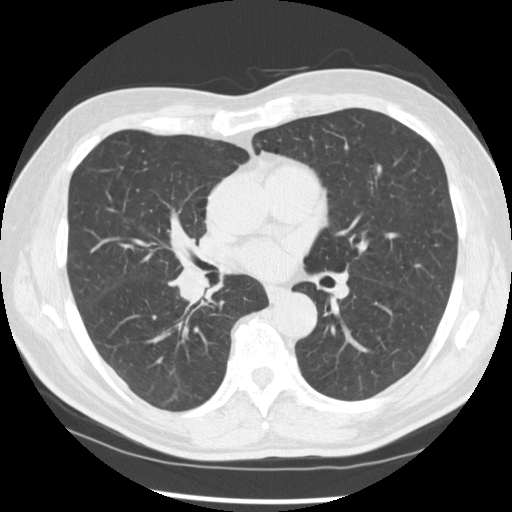
Low-dose screening chest CT, one axial slice; position 148 of 277 along the scan axis; lung window (W 1500 / L -600 HU); 512 × 512 image matrix, field of view 365 × 365 mm.
Structures marked on this image (manually delineated by an expert):
- lesion 1 (tumor, middle lobe of right lung): bounding box [x1, y1, x2, y2] px = [176, 263, 209, 302]